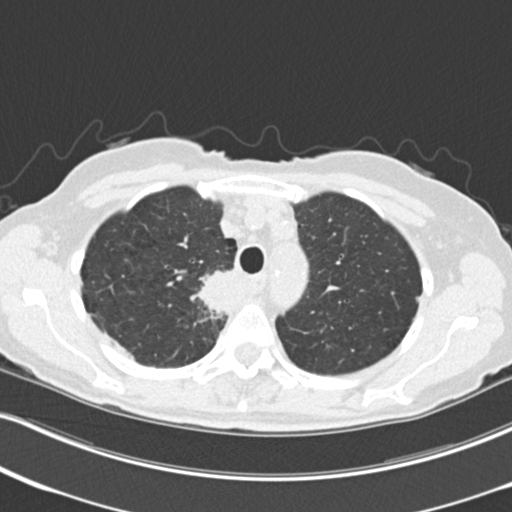
Low-dose screening chest CT, one axial slice. Position 175 of 226 along the scan axis. 120 kVp. Lung window (W 1500 / L -600 HU). 512 × 512 image matrix.
Structures marked on this image (expert manual segmentation):
- lesion 1 (tumor, mediastinum): bounding box (x1, y1, x2, y2) in pixels: (190, 271, 233, 317)